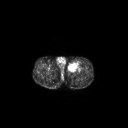
FDG PET of an extremity soft-tissue mass (from a PET/CT study), one axial slice; 3.27 mm slice thickness; 128 × 128 image matrix, field of view 700 × 700 mm. Male patient, age 63 years. From the clinical record (not read from this slice): histological type: pleiomorphic liposarcoma; grade: high; site of the primary tumour: left thigh.
Structures marked on this image (expert contour drawn on MRI and transferred to this co-registered scan by the dataset authors):
- gross tumour volume including surrounding oedema: box from (x=68, y=61) to (x=80, y=71) px
- gross tumour volume (mass): (x=68, y=63)–(x=77, y=70)